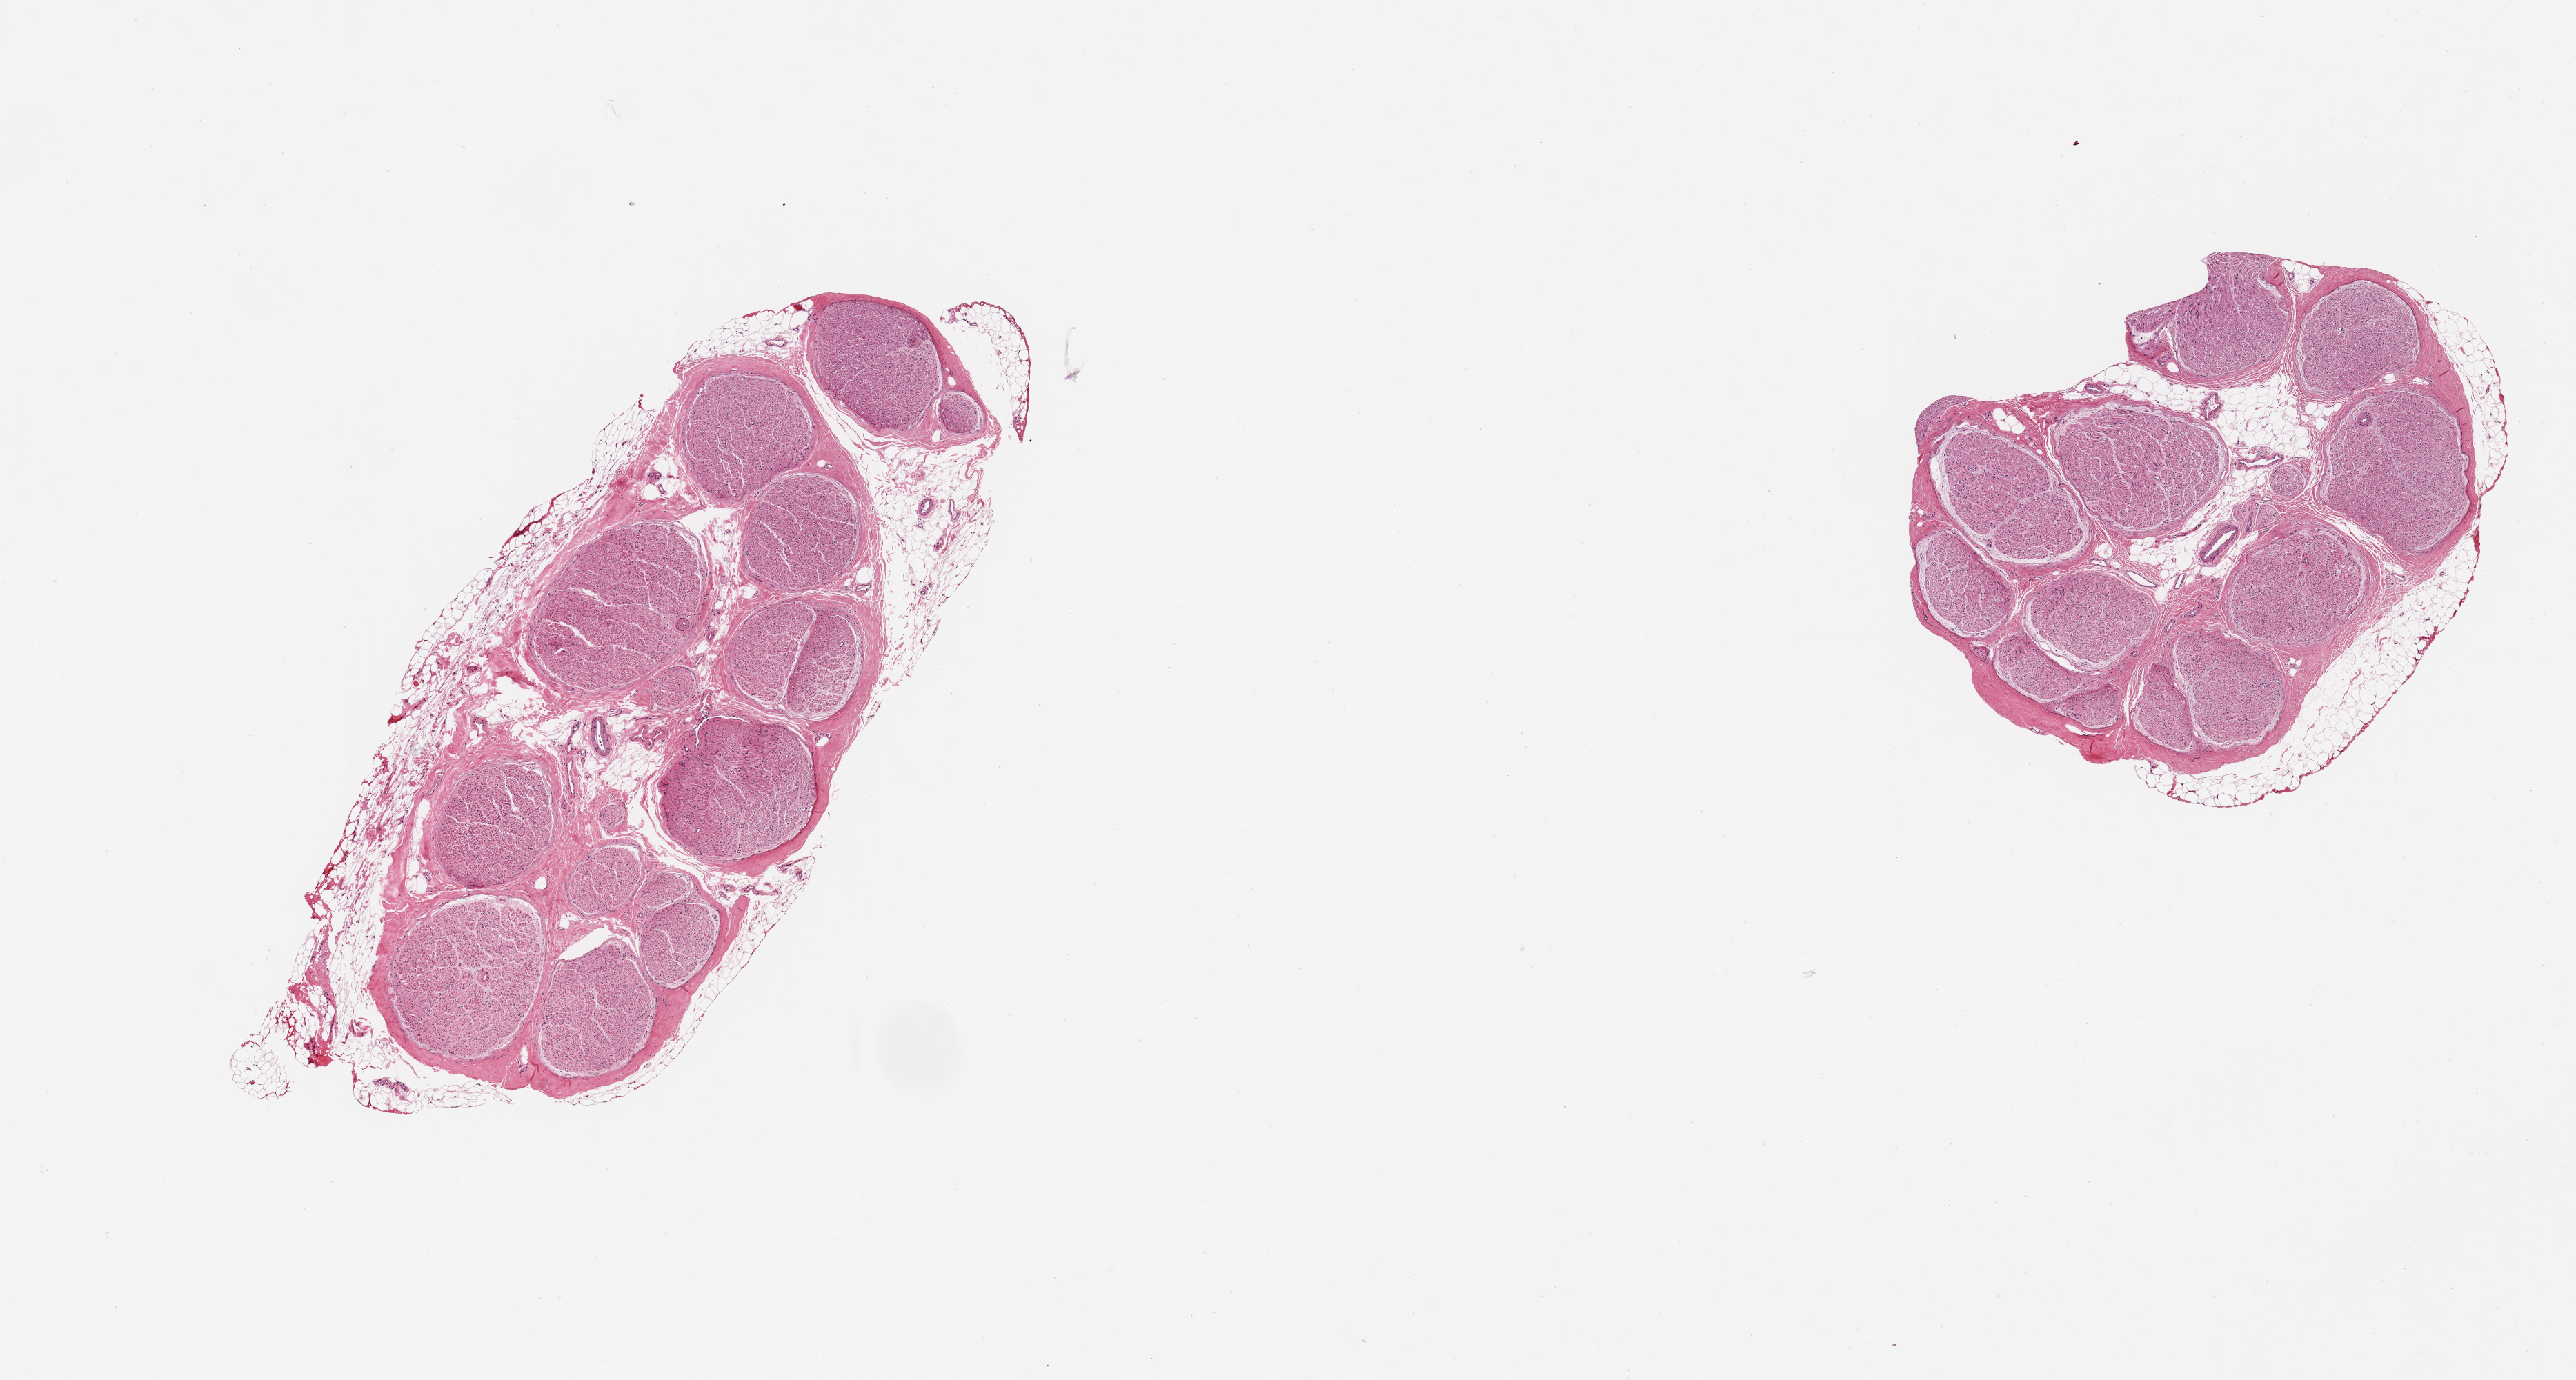
Hematoxylin and eosin (H&E) whole-slide image, whole scanned area (about 14.8 x 7.9 mm) shown as a low-resolution overview; PAXgene-fixed, paraffin-embedded tissue; target tissue: tibial nerve; donor tissue sample. Donor: male.
Reviewer comment on this tissue sample: 2 pieces; 10% external fat content.